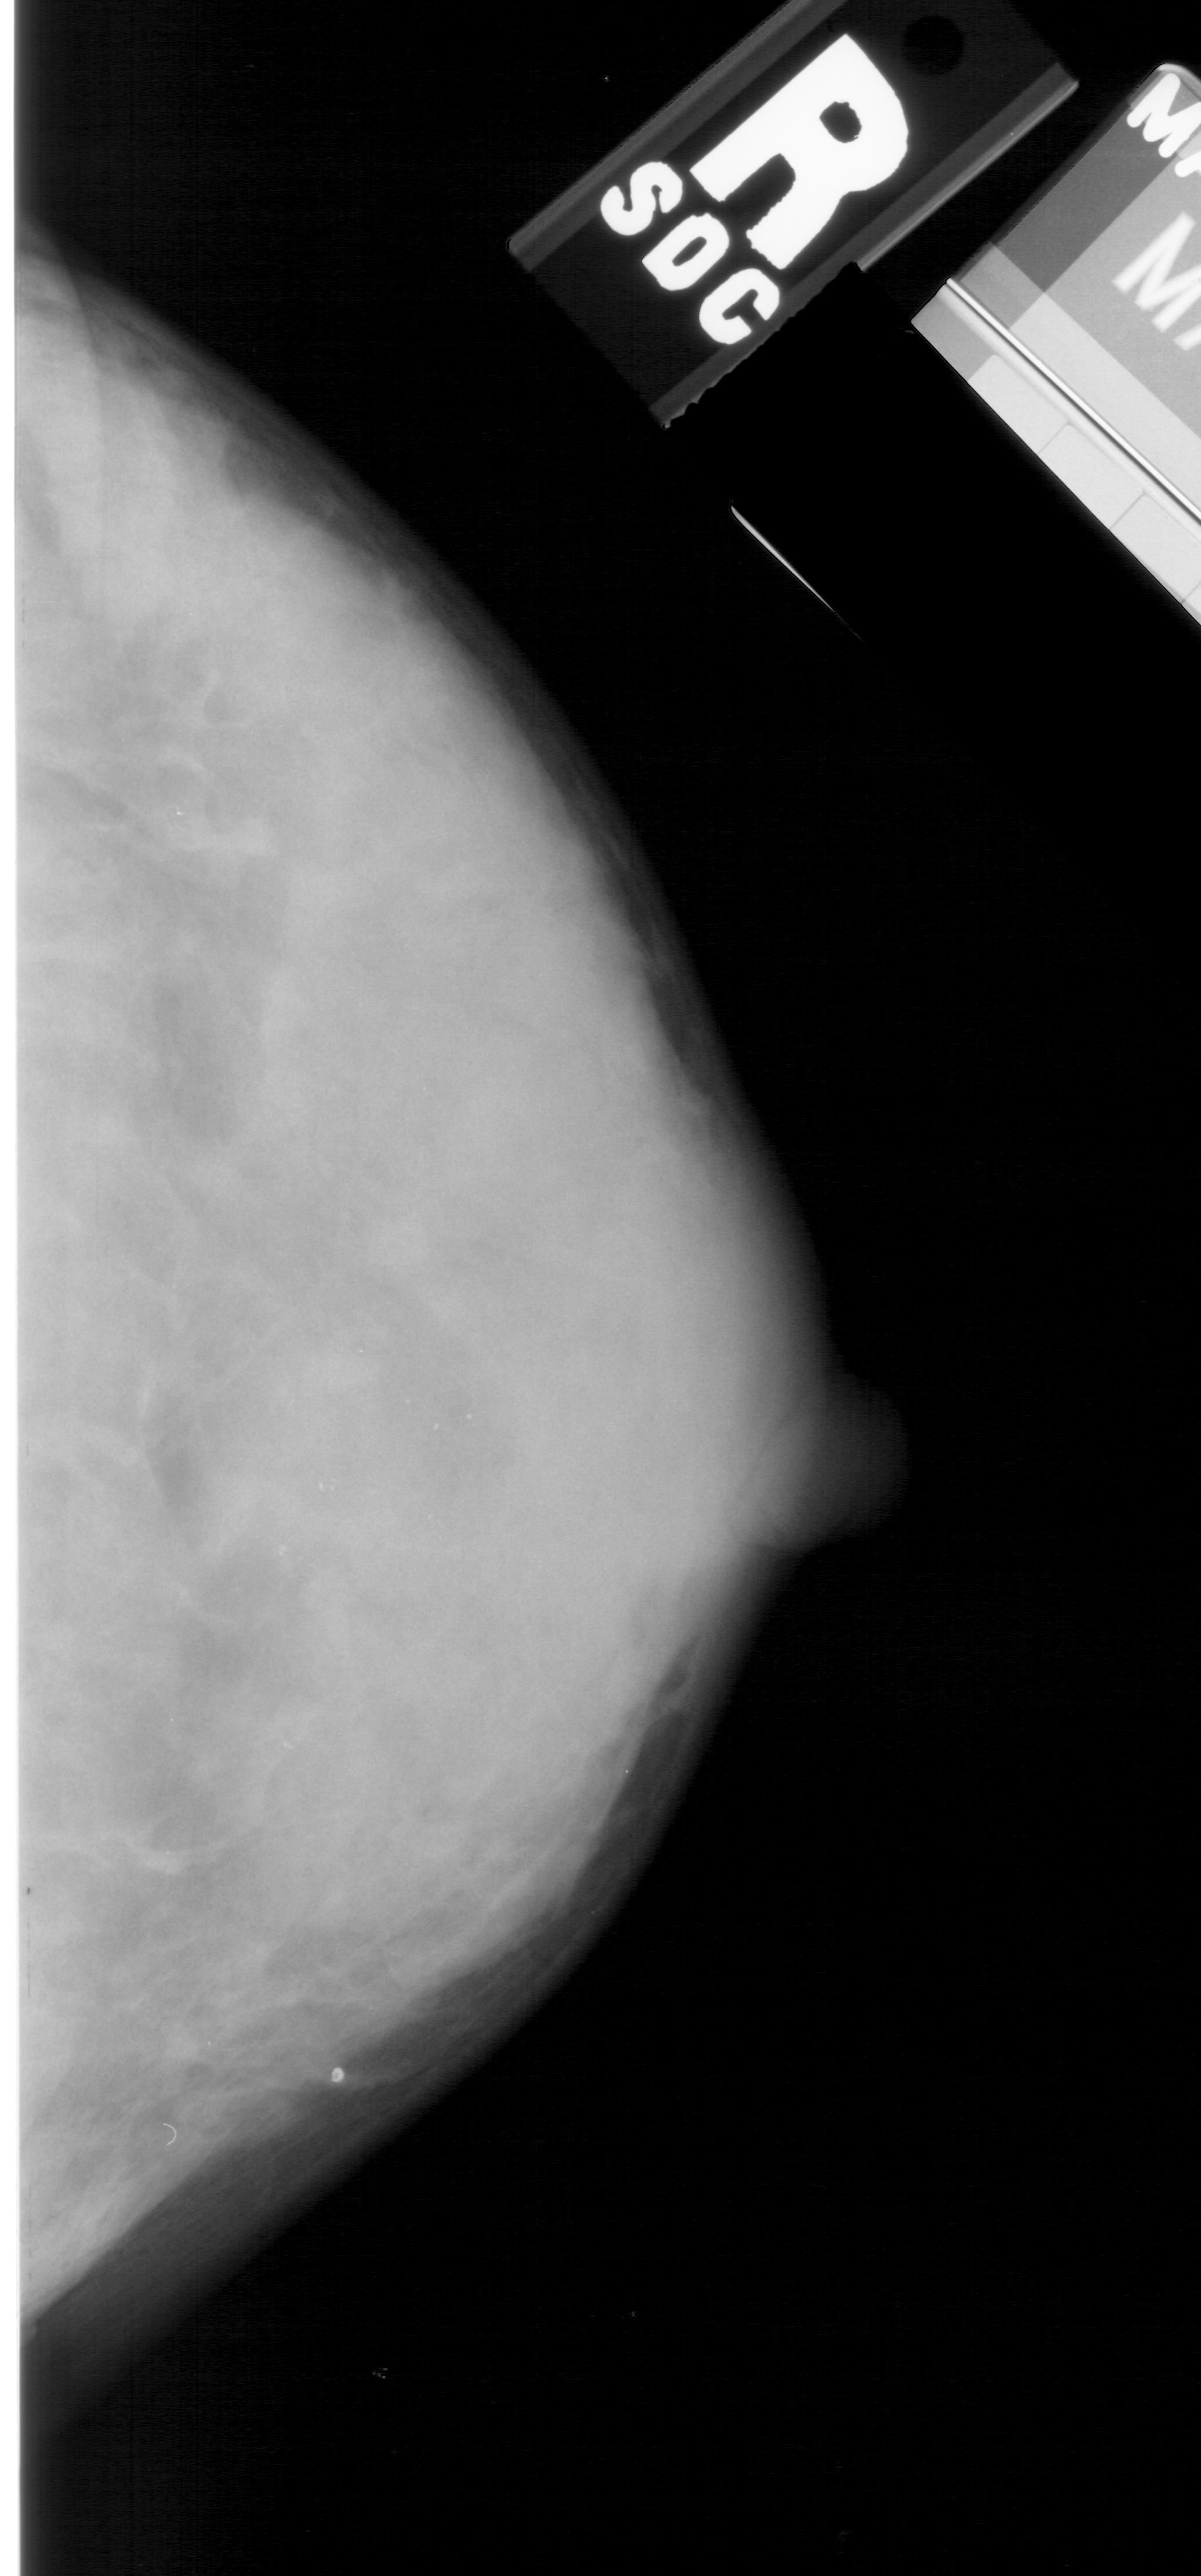
Digitized screen-film mammogram. Right breast. Craniocaudal (CC) view. BI-RADS breast density category 4 (scale 1–4). 1201 × 2576 image matrix.
Expert-marked regions of interest on this film, with their recorded descriptors:
- calcifications, morphology pleomorphic, distribution segmental; BI-RADS assessment category 4; pathology (as recorded): benign: bounding box [x1, y1, x2, y2] px = [257, 1385, 495, 1596]